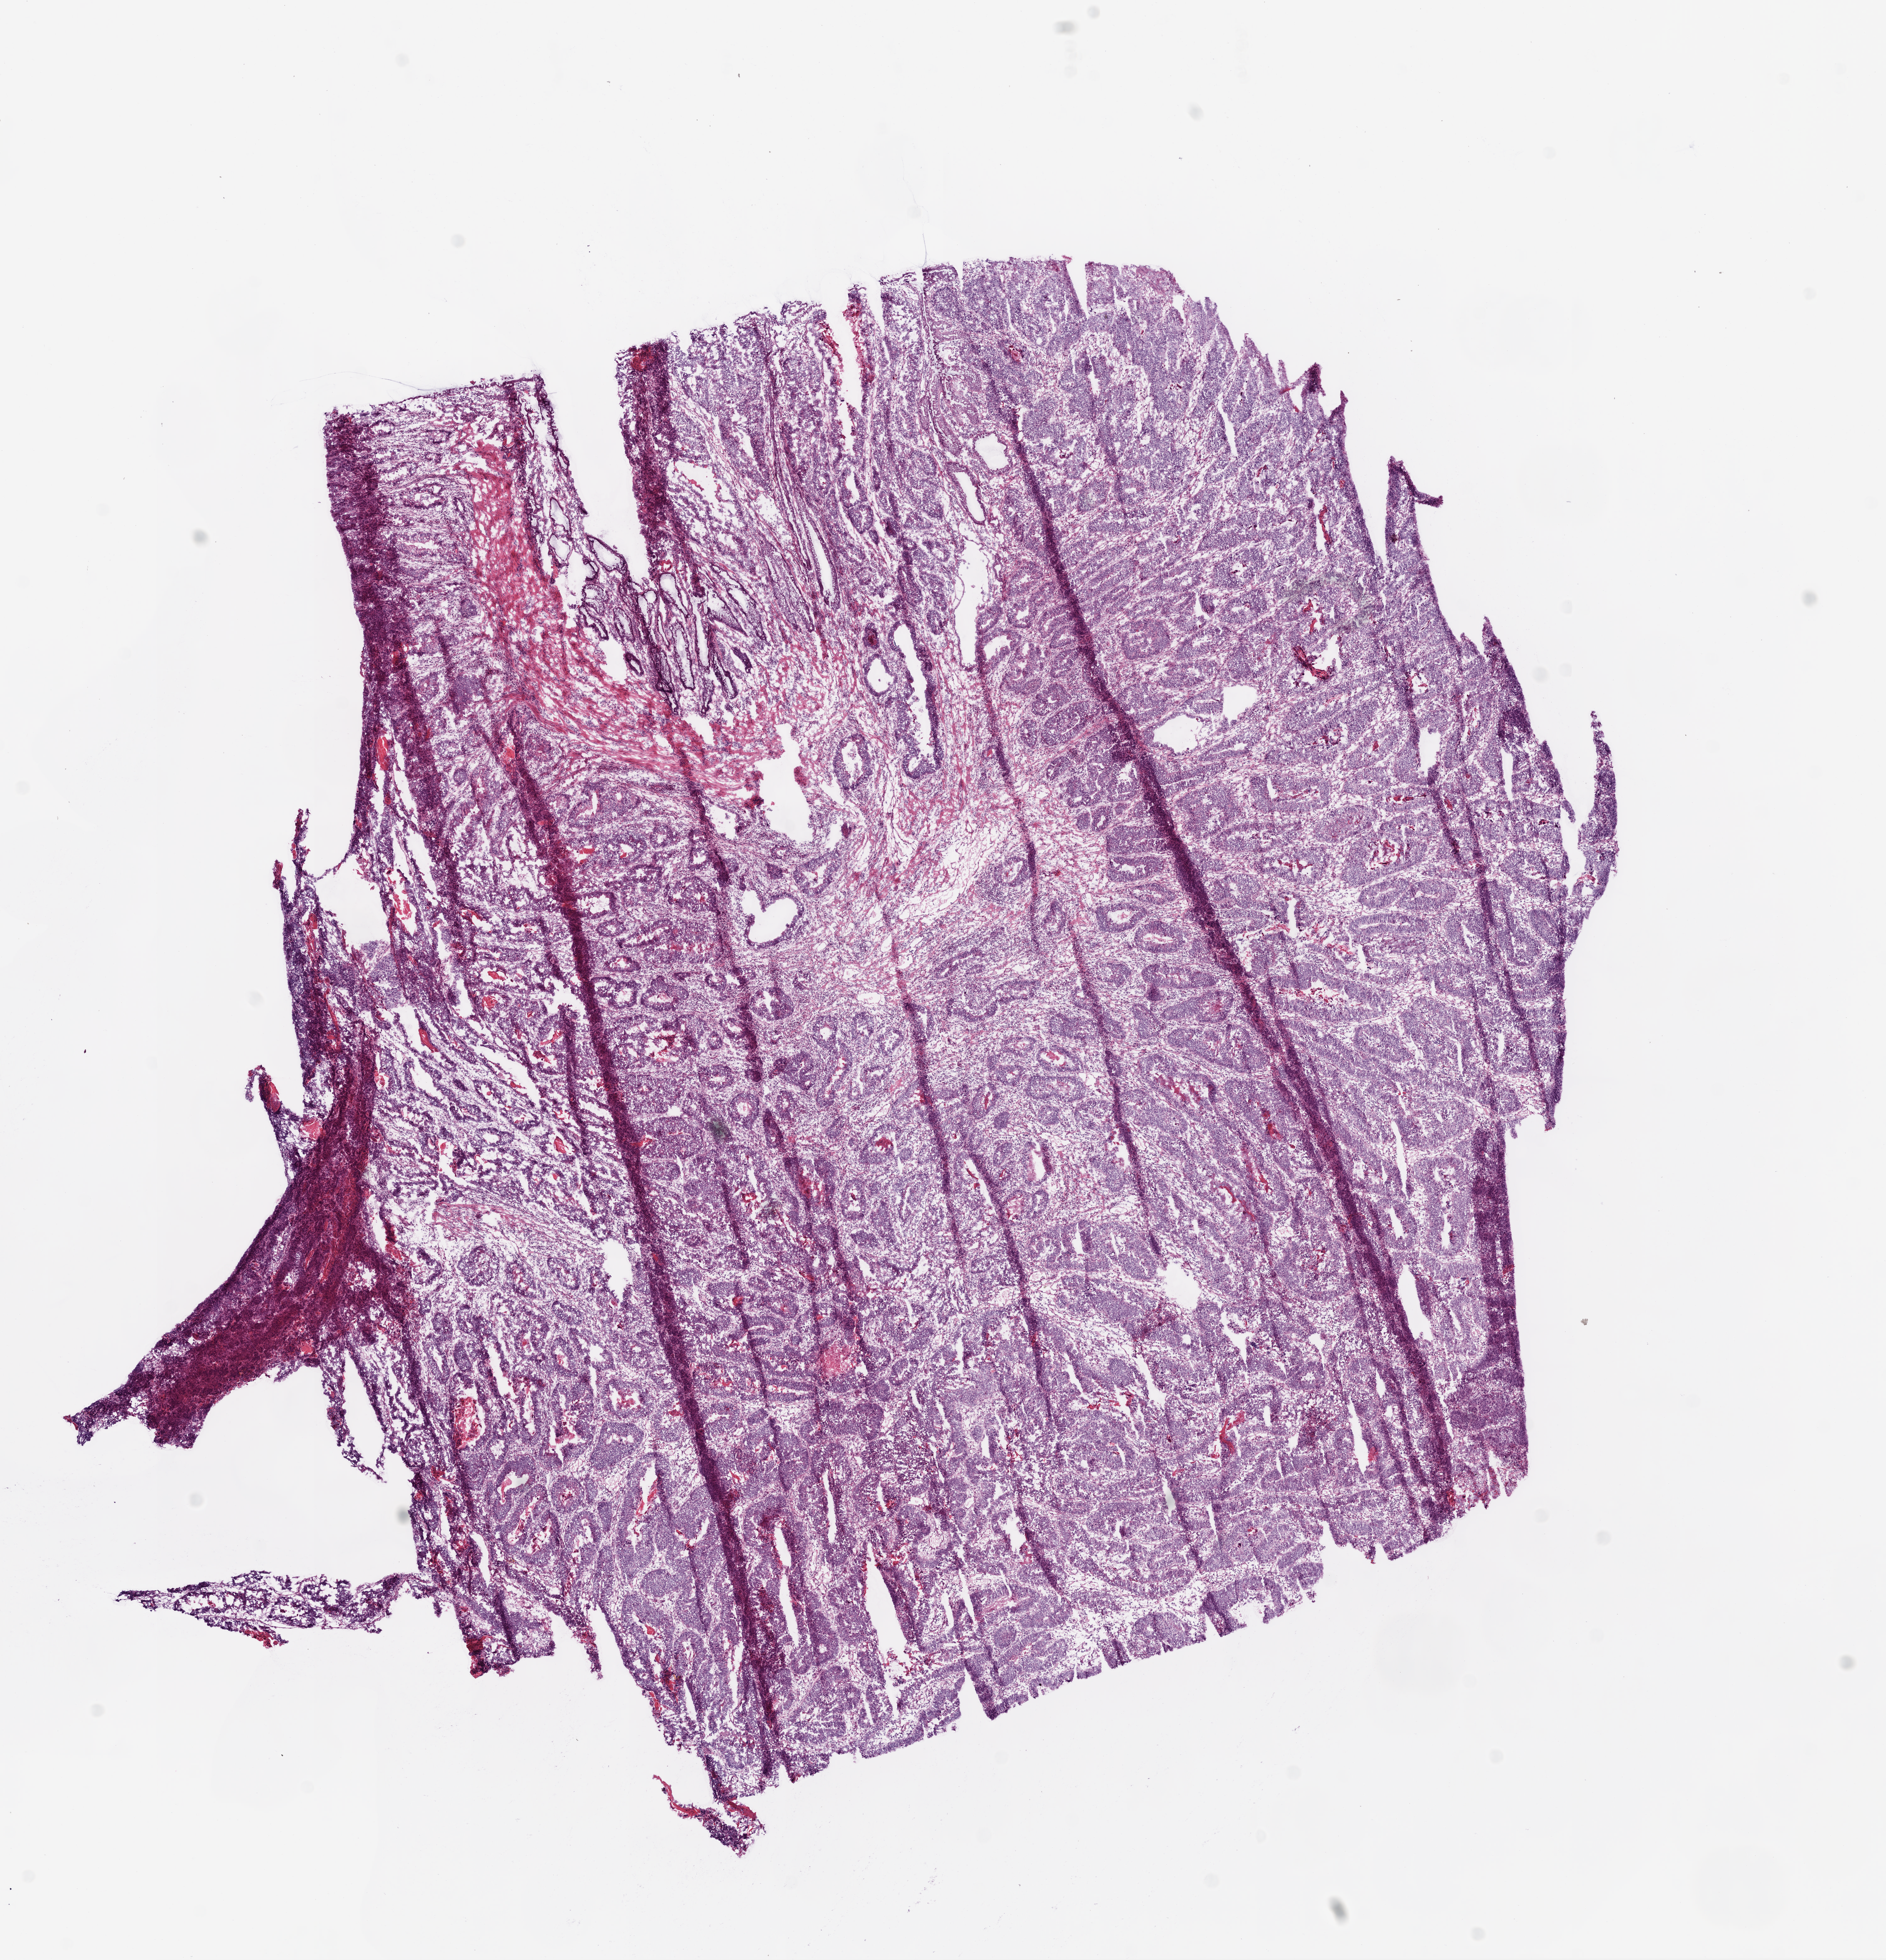
Whole-slide histology image, H&E, a low-resolution overview of the entire scanned area, about 12.0 x 12.5 mm (acquisition: 20x scan); frozen section from the bottom of the tissue portion; rectum, primary tumour sample. Female, age 72 years at initial diagnosis. Composition of this section per pathologist review: tumour cells 85%, tumour nuclei 85%, normal cells 2%, stromal cells 12%, necrosis 1%. Inflammatory infiltration, as recorded: lymphocyte infiltration 5%.
• diagnosis: Adenocarcinoma, NOS
• AJCC pathologic stage: IIA